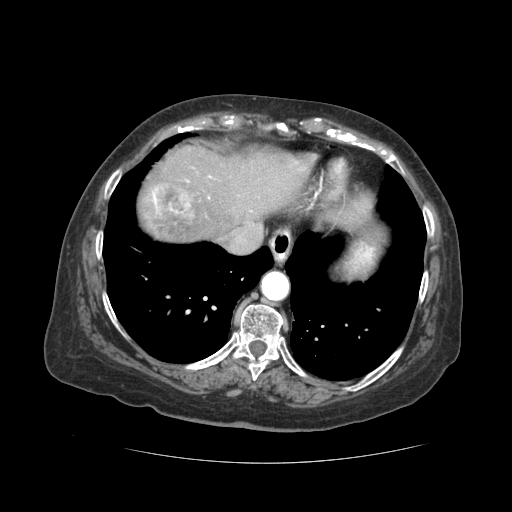
Contrast-enhanced abdominal CT (liver protocol), one axial slice. Reconstruction kernel STANDARD. Soft-tissue window (W 400 / L 40 HU). 2.5 mm slice thickness. 512 × 512 image matrix, field of view 380 × 380 mm. Case-level facts recorded for this patient, not image findings: diagnosis: hepatocellular carcinoma (patient treated with transarterial chemoembolisation; whether this scan precedes or follows treatment is not stated here); TNM stage (as recorded): Stage-I.
Structures marked on this image (semi-automatic segmentation, software-assisted and operator-edited):
- liver parenchyma outside the tumour (the mass and vessels are separate outlines, so this box may not span the whole liver): box from (x=138, y=145) to (x=315, y=242) px
- mass: (x=148, y=184)–(x=194, y=235)
- liver vessels: (x=186, y=176)–(x=211, y=183)